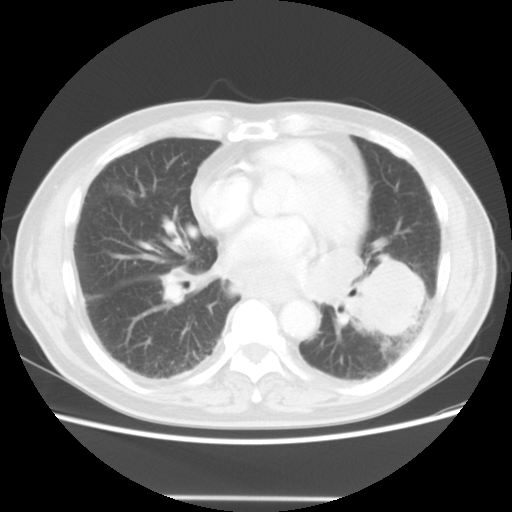
Chest CT, one axial slice; reconstruction kernel STANDARD; 140 kVp; lung window (W 1500 / L -600 HU); 512 × 512 image matrix, field of view 360 × 360 mm. Patient: male, 66 years. From the clinical record (not read from this slice): clinical TNM (as recorded): T4 N3 M0; histopathological grade: G3.
Structures marked on this image (rectangle marked by the reading radiologist):
- lung tumour (recorded histology: small cell carcinoma): bounding box <337,251,433,346> (left, top, right, bottom; pixels)